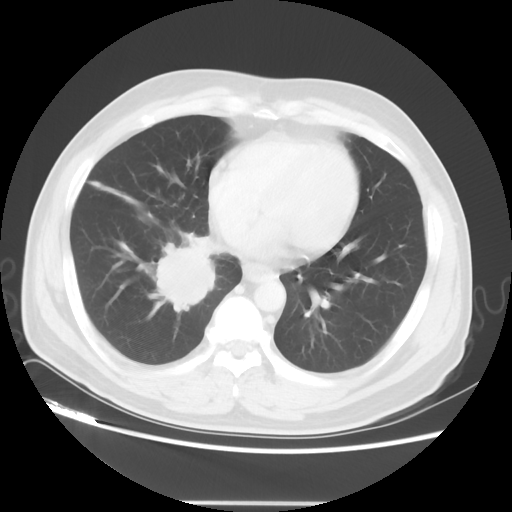
Chest CT, one axial slice. Lung window (W 1500 / L -600 HU). 5 mm slice thickness. 512 × 512 image matrix, field of view 390 × 390 mm. Patient: male, 53 years. Case-level facts recorded for this patient, not image findings: clinical TNM (as recorded): T2 N3 M0.
Outlined on this slice (rectangle marked by the reading radiologist):
- lung tumour (recorded histology: small cell carcinoma): bounding box [x1, y1, x2, y2] px = [151, 232, 227, 319]